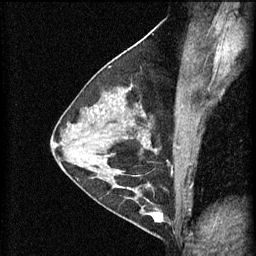
Breast MRI (dynamic contrast-enhanced), one sagittal slice. Position 34 of 60 along the scan axis. 3 images stored at this slice position (order not interpretable as contrast timing). 1.5 T. TE 4.2 ms, TR 11 ms. 256 × 256 image matrix. Patient: female, 29 years.
Outlined on this slice (semi-automatically segmented with operator editing):
- analysis volume of interest (the breast-tissue region the enhancement analysis was run in; not a lesion): bounding box <105,172,165,227> (left, top, right, bottom; pixels)
- tumour enhancement mask (voxels above the 70 % enhancement threshold inside the analysis volume of interest): <112,172,165,223>